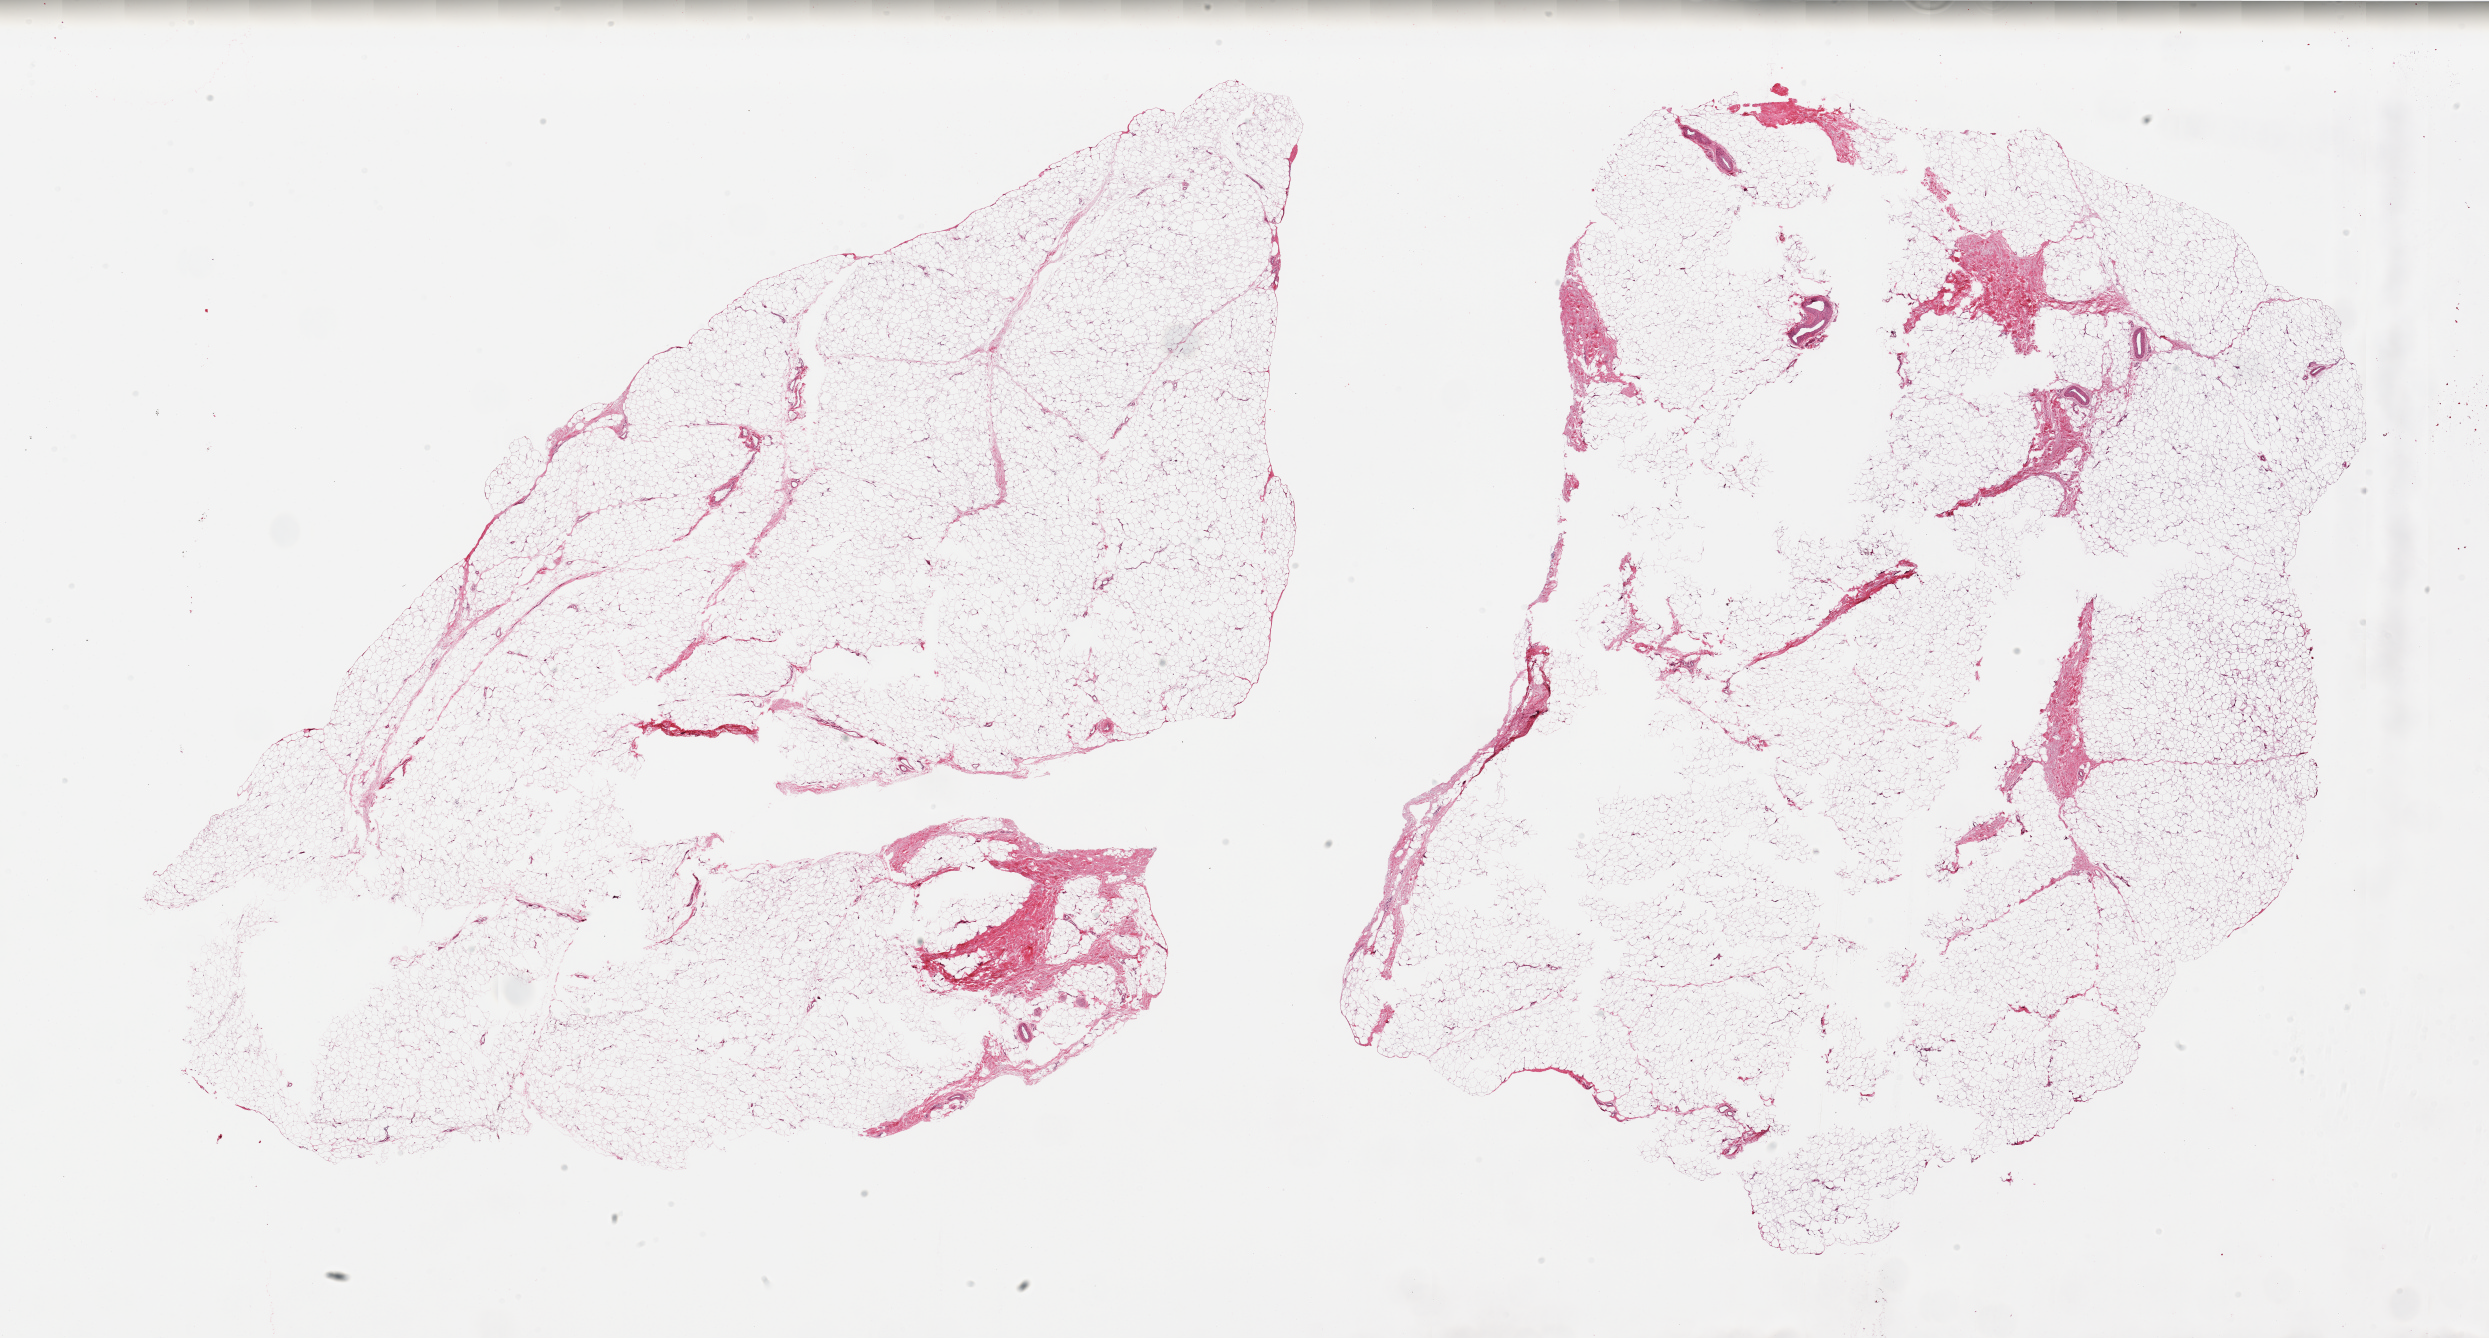
Digitized H&E-stained section, brightfield, shown as a low-resolution overview of the whole scanned area (about 39.4 x 21.2 mm). PAXgene-fixed paraffin-embedded (PFPE) section. Section of adipose tissue (target tissue). Donor tissue sample. Donor sex: male.
Pathologist's review note for this sample: 2 pieces; ~10% fibrovascular component, over-sized specimens with central defects (?poor fixation).